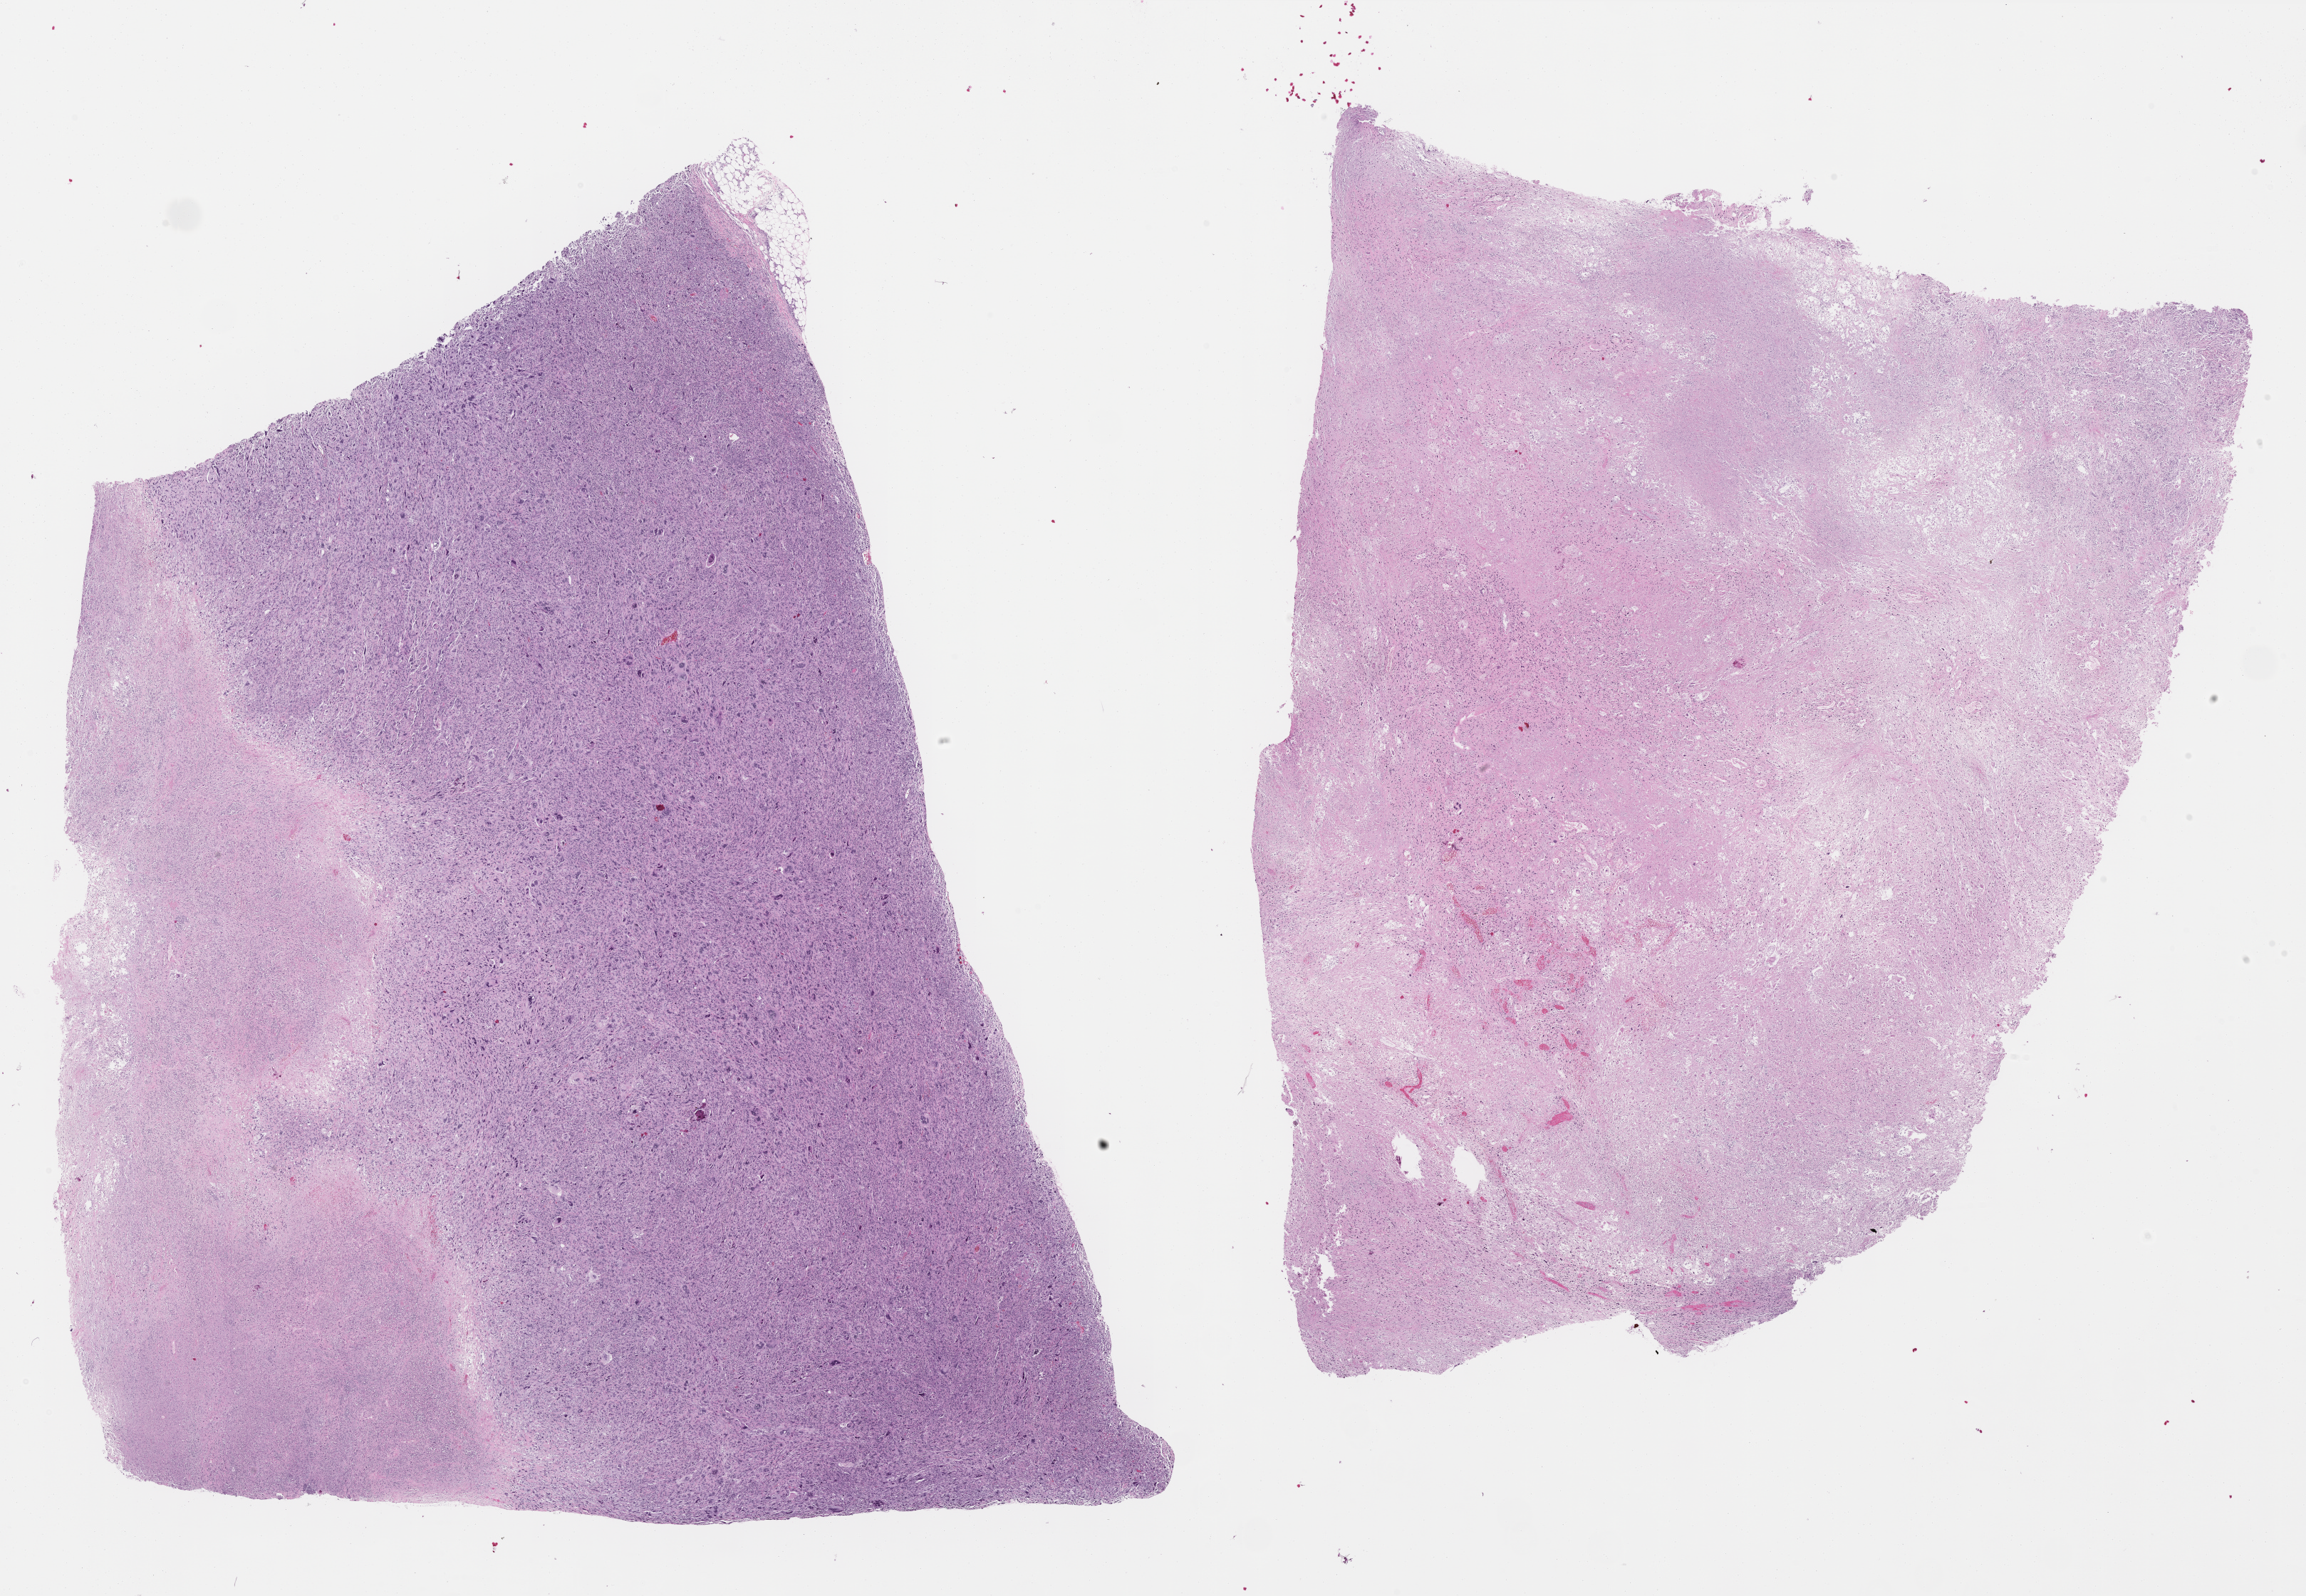
Whole-slide histology image, H&E-stained, shown as a low-resolution overview of the whole scanned area (about 26.0 x 18.0 mm, acquisition: 40x scan), formalin-fixed paraffin-embedded (FFPE) diagnostic section, primary tumour sample from the connective, subcutaneous and other soft tissues. Male patient; age at initial diagnosis 71 years.
* diagnosis: Undifferentiated sarcoma (connective, subcutaneous and other soft tissues of trunk, NOS)